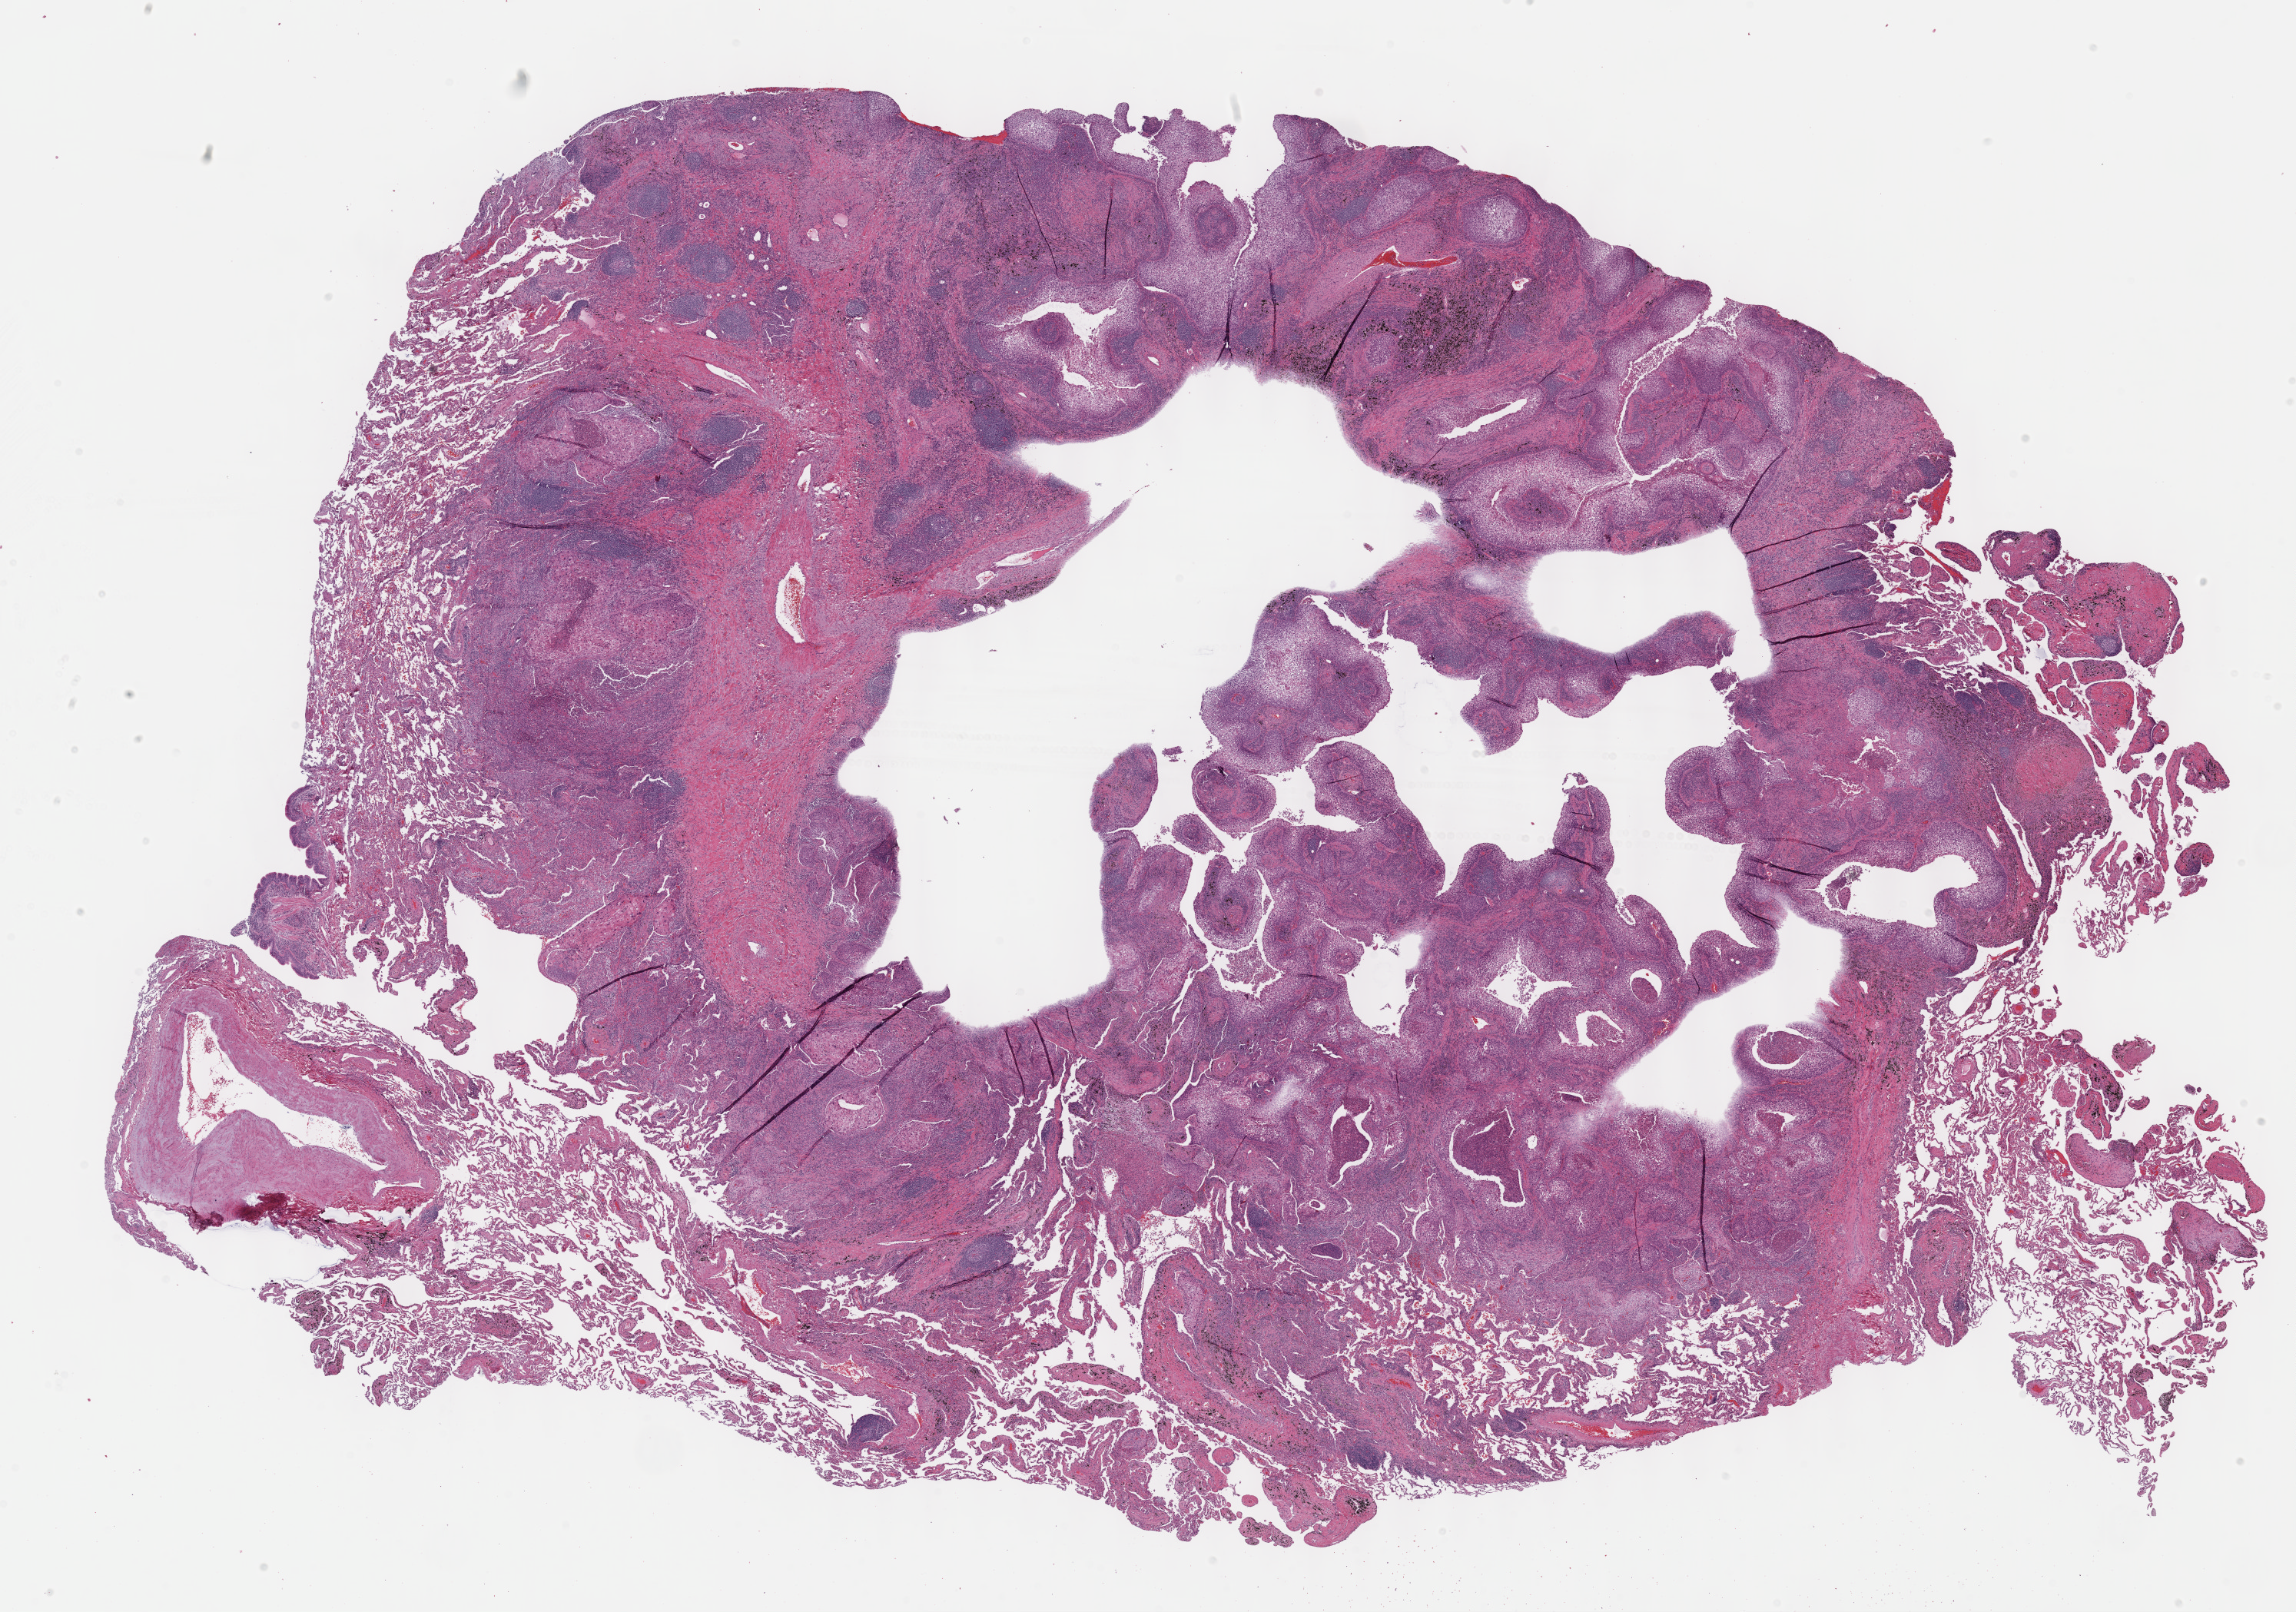
Hematoxylin and eosin (H&E) stained whole-slide image — whole scanned area (about 24.1 x 17.0 mm) shown as a low-resolution overview, formalin-fixed paraffin-embedded (FFPE) diagnostic section, primary tumour sample from the lung. Male patient; age at initial diagnosis 73 years.
• AJCC pathologic stage: IB
• laterality: right
• histologic diagnosis: Squamous cell carcinoma, NOS